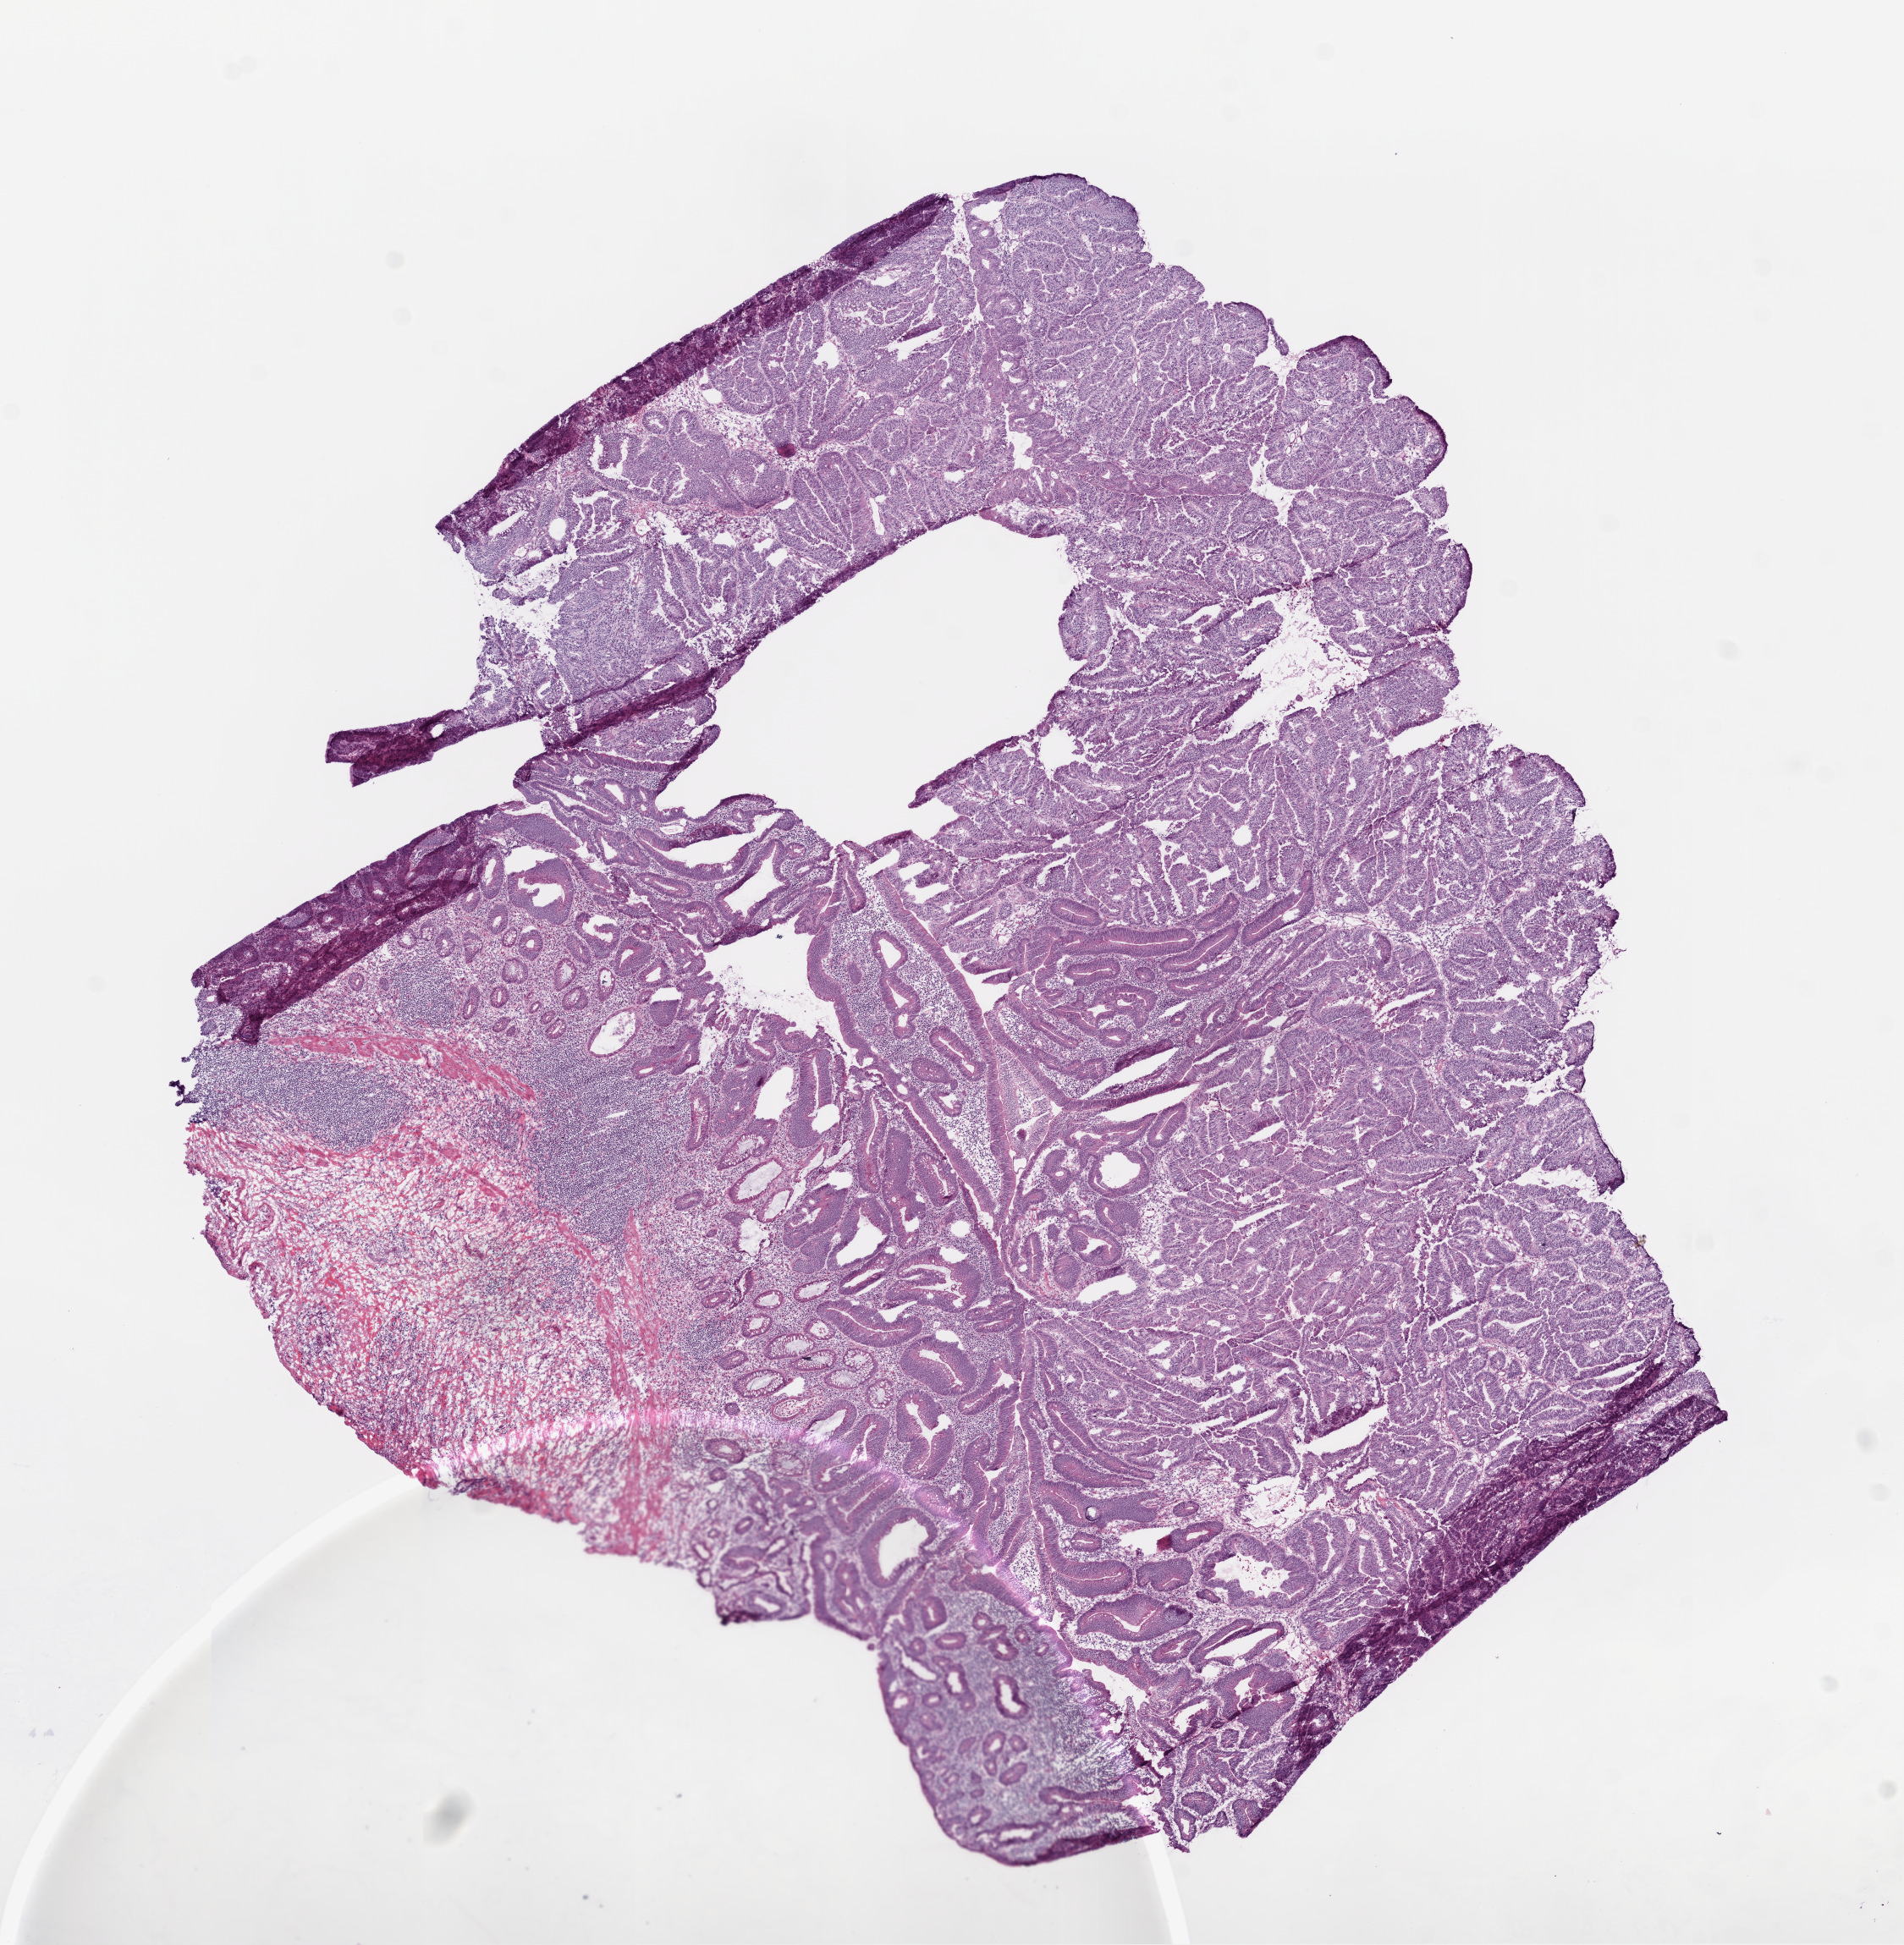
Whole-slide histology image, H&E — low-resolution overview of the scanned area, about 9.0 x 9.2 mm (acquisition: 20x scan). Frozen section. Sample: primary tumour, colon. Male, age 80 years at initial diagnosis. Composition of this section per pathologist review: tumour cells 80%, tumour nuclei 90%, normal cells 0%, stromal cells 20%, necrosis 0%. Inflammatory infiltration, as recorded: lymphocyte infiltration 5%.
• lymph nodes positive (case pathology): 0 of 24 examined
• histologic diagnosis: Adenocarcinoma, NOS (ascending colon)
• AJCC pathologic stage: I (6th edition)